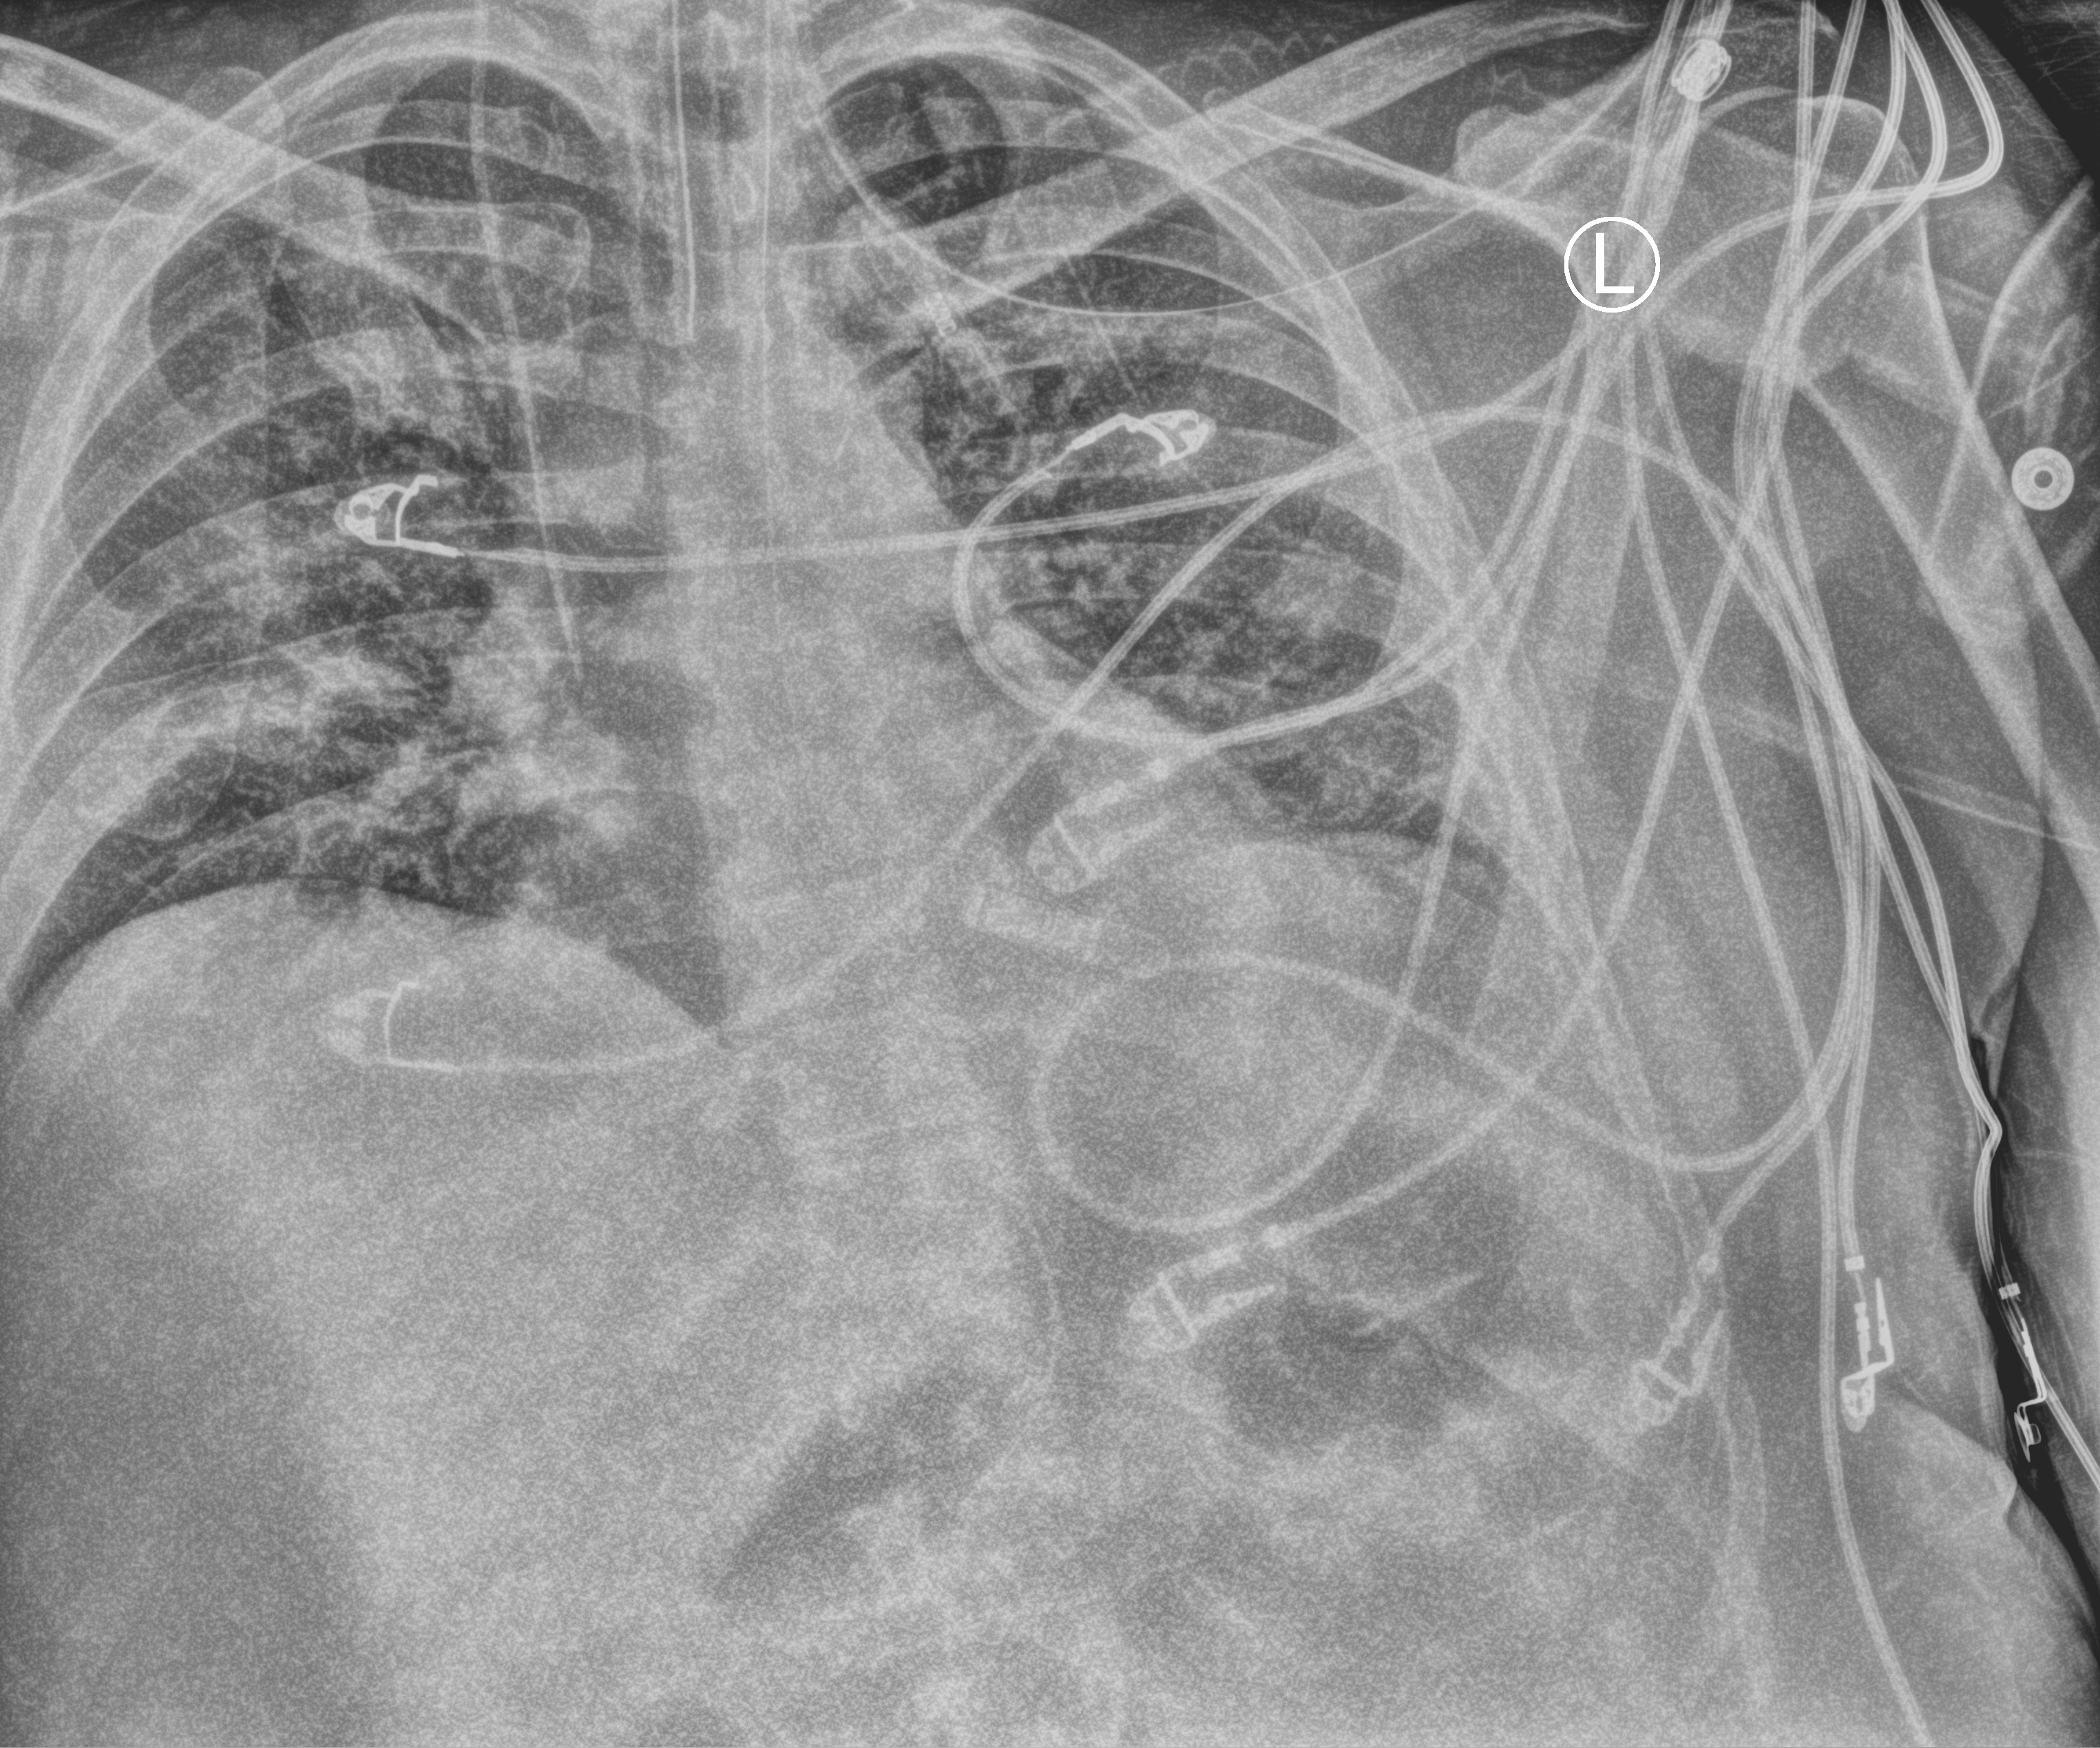
Portable chest radiograph; anteroposterior (AP) projection. Male patient hospitalised with COVID-19, age 18–59 years.
Admission-level facts for this patient (not findings on this image; timing relative to this image not recorded): mechanically ventilated during this hospital stay: yes.